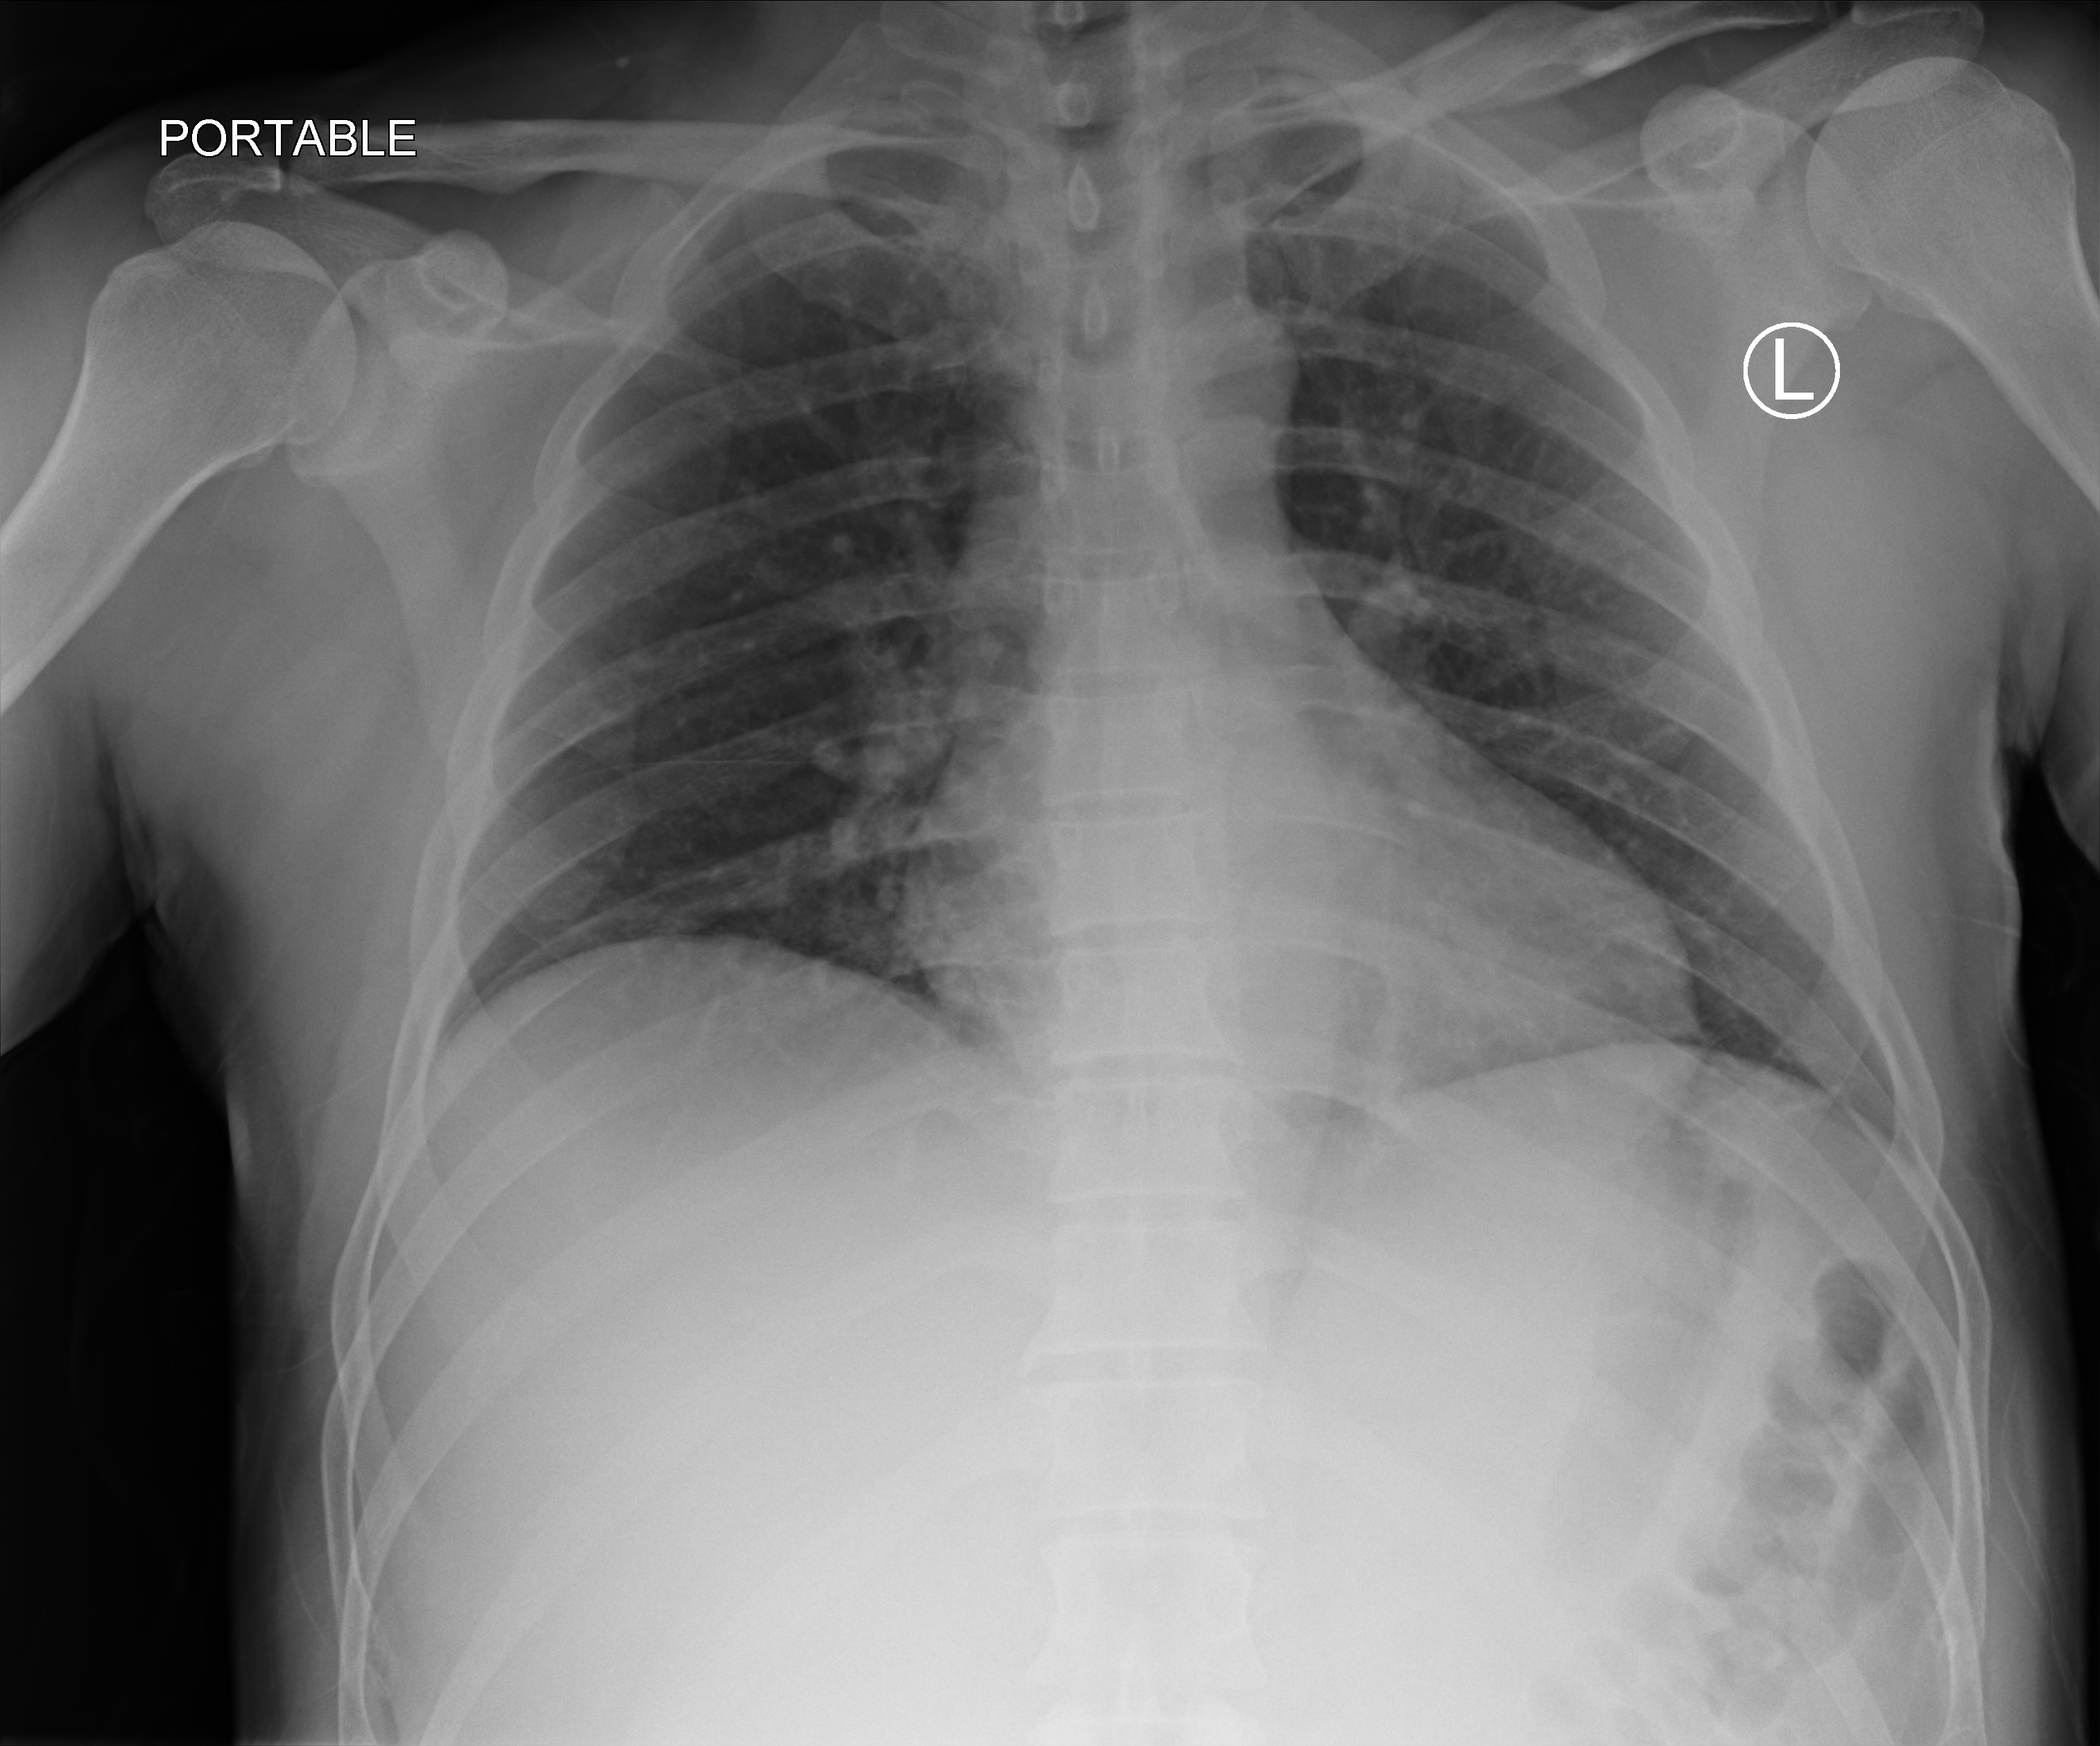
Bedside chest radiograph (computed radiography), anteroposterior (AP) projection. Male patient hospitalised with COVID-19, age 18–59 years.
From the hospital-stay record, not from the radiograph (when in the stay this image was taken is not recorded): mechanically ventilated during this hospital stay: no; length of hospital stay: 5 days.